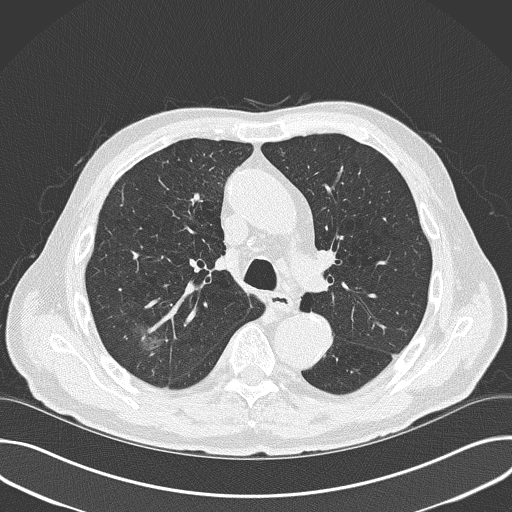
Low-dose screening chest CT, axial slice; first (baseline) screen; lung window (W 1500 / L -600 HU); 2 mm slice thickness; 120 kVp; slice 110 of 177 in the series. Male, age 74 years at enrolment. Former smoker at enrolment.
Lesion marked by an expert reader, bounding box <125,316,178,367> (left, top, right, bottom; pixels). The screening reader recorded 3 non-calcified nodules or masses ≥4 mm on this exam; which of them this box marks is not recorded. Lung cancer was diagnosed 215 days after this screen: small cell carcinoma, NOS, right upper lobe, stage IV (AJCC 6th edition), 15 mm at pathology.